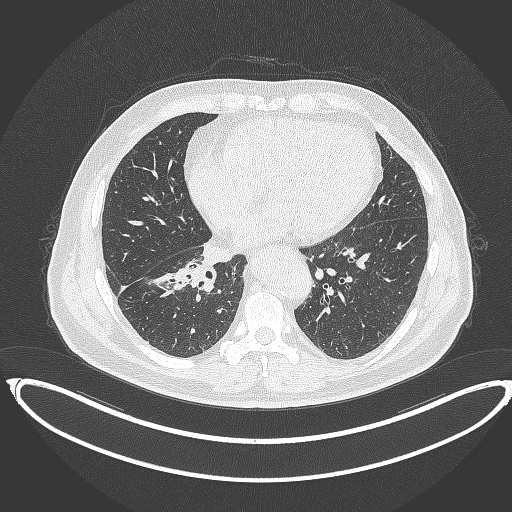
Chest CT, one axial slice. Slice 159 of 387 in the series (ordered by position). Reconstruction kernel B70f. Lung window (W 1500 / L -600 HU). 512 × 512 image matrix, field of view 448 × 448 mm. Male patient, age 61 years. Case-level facts recorded for this patient, not image findings: clinical TNM (as recorded): T1b N1 M0.
Annotated regions visible in this slice (bounding box drawn by a radiologist):
- lung tumour (recorded histology: squamous cell carcinoma): bounding box <173,260,217,294> (left, top, right, bottom; pixels)